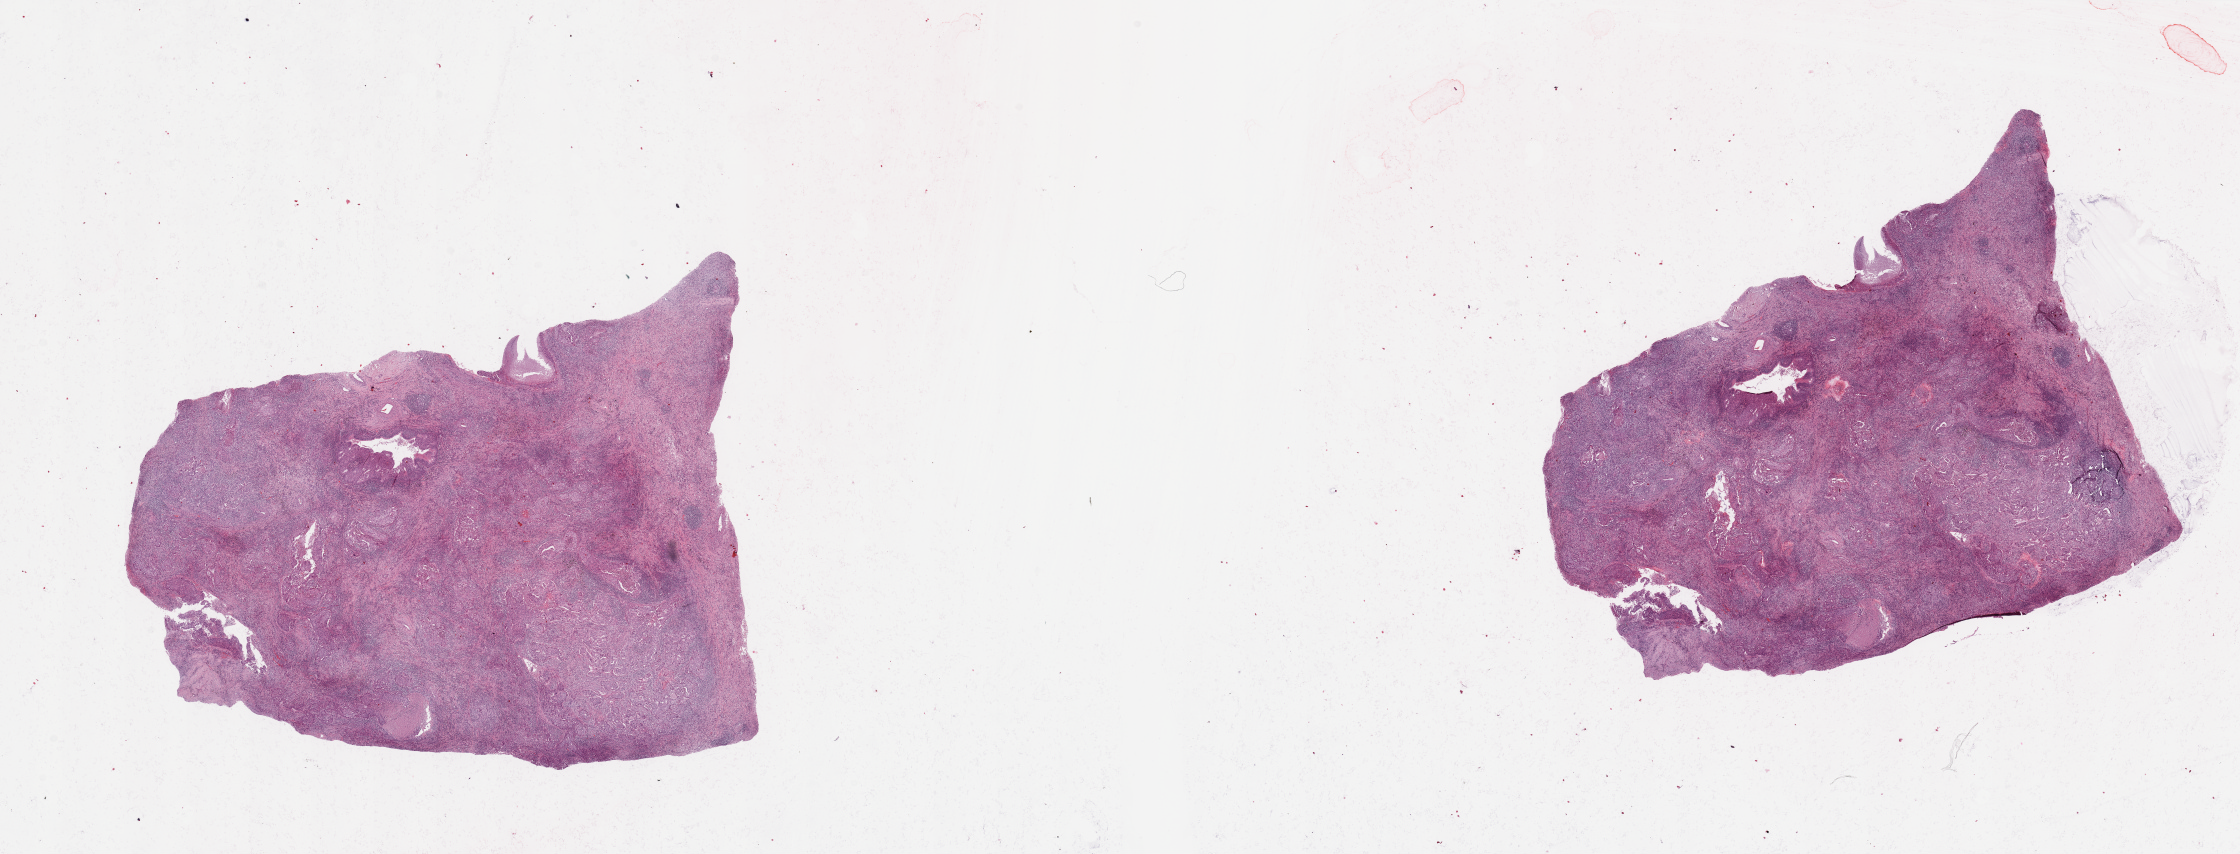
Whole-slide histology image, Hematoxylin and eosin (H&E) stained — shown as a low-resolution overview of the whole scanned area (about 35.4 x 13.5 mm, acquisition: 20x scan), lung, tumour tissue. 57-year-old male patient. Histologic grade: G2 (moderately differentiated).
Diagnosis: Squamous cell carcinoma, NOS. Primary tumour site (as recorded): right lower lobe. AJCC pathologic stage: IIB.